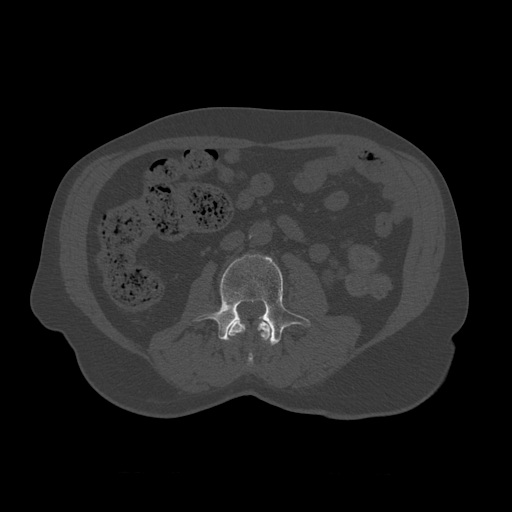
CT including the spine, one axial slice. Position 309 of 450 along the scan axis. 120 kVp. Bone window (W 1800 / L 400 HU). 1.25 mm slice thickness. 512 × 512 image matrix, field of view 405 × 405 mm. Patient age 75 years. From the clinical record (not read from this slice): primary cancer: prostate.
Structures marked on this image (semi-automatic segmentation, software-assisted and operator-edited):
- L2 vertebra: bounding box <228,319,272,366> (left, top, right, bottom; pixels)
- L3 vertebra: <194,254,311,346>